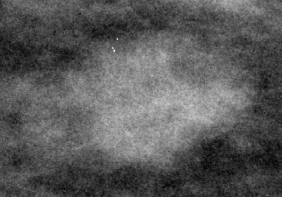
Crop from a digitized film mammogram around one marked abnormality; right breast; CC view; BI-RADS breast density category 2 (scale 1–4).
Marked abnormality: mass, shape lobulated, margins circumscribed / ill defined; BI-RADS assessment category 4; subtlety rating 4 on a 1 (subtle) to 5 (obvious) scale; pathology result (as recorded, not read from the image): benign.